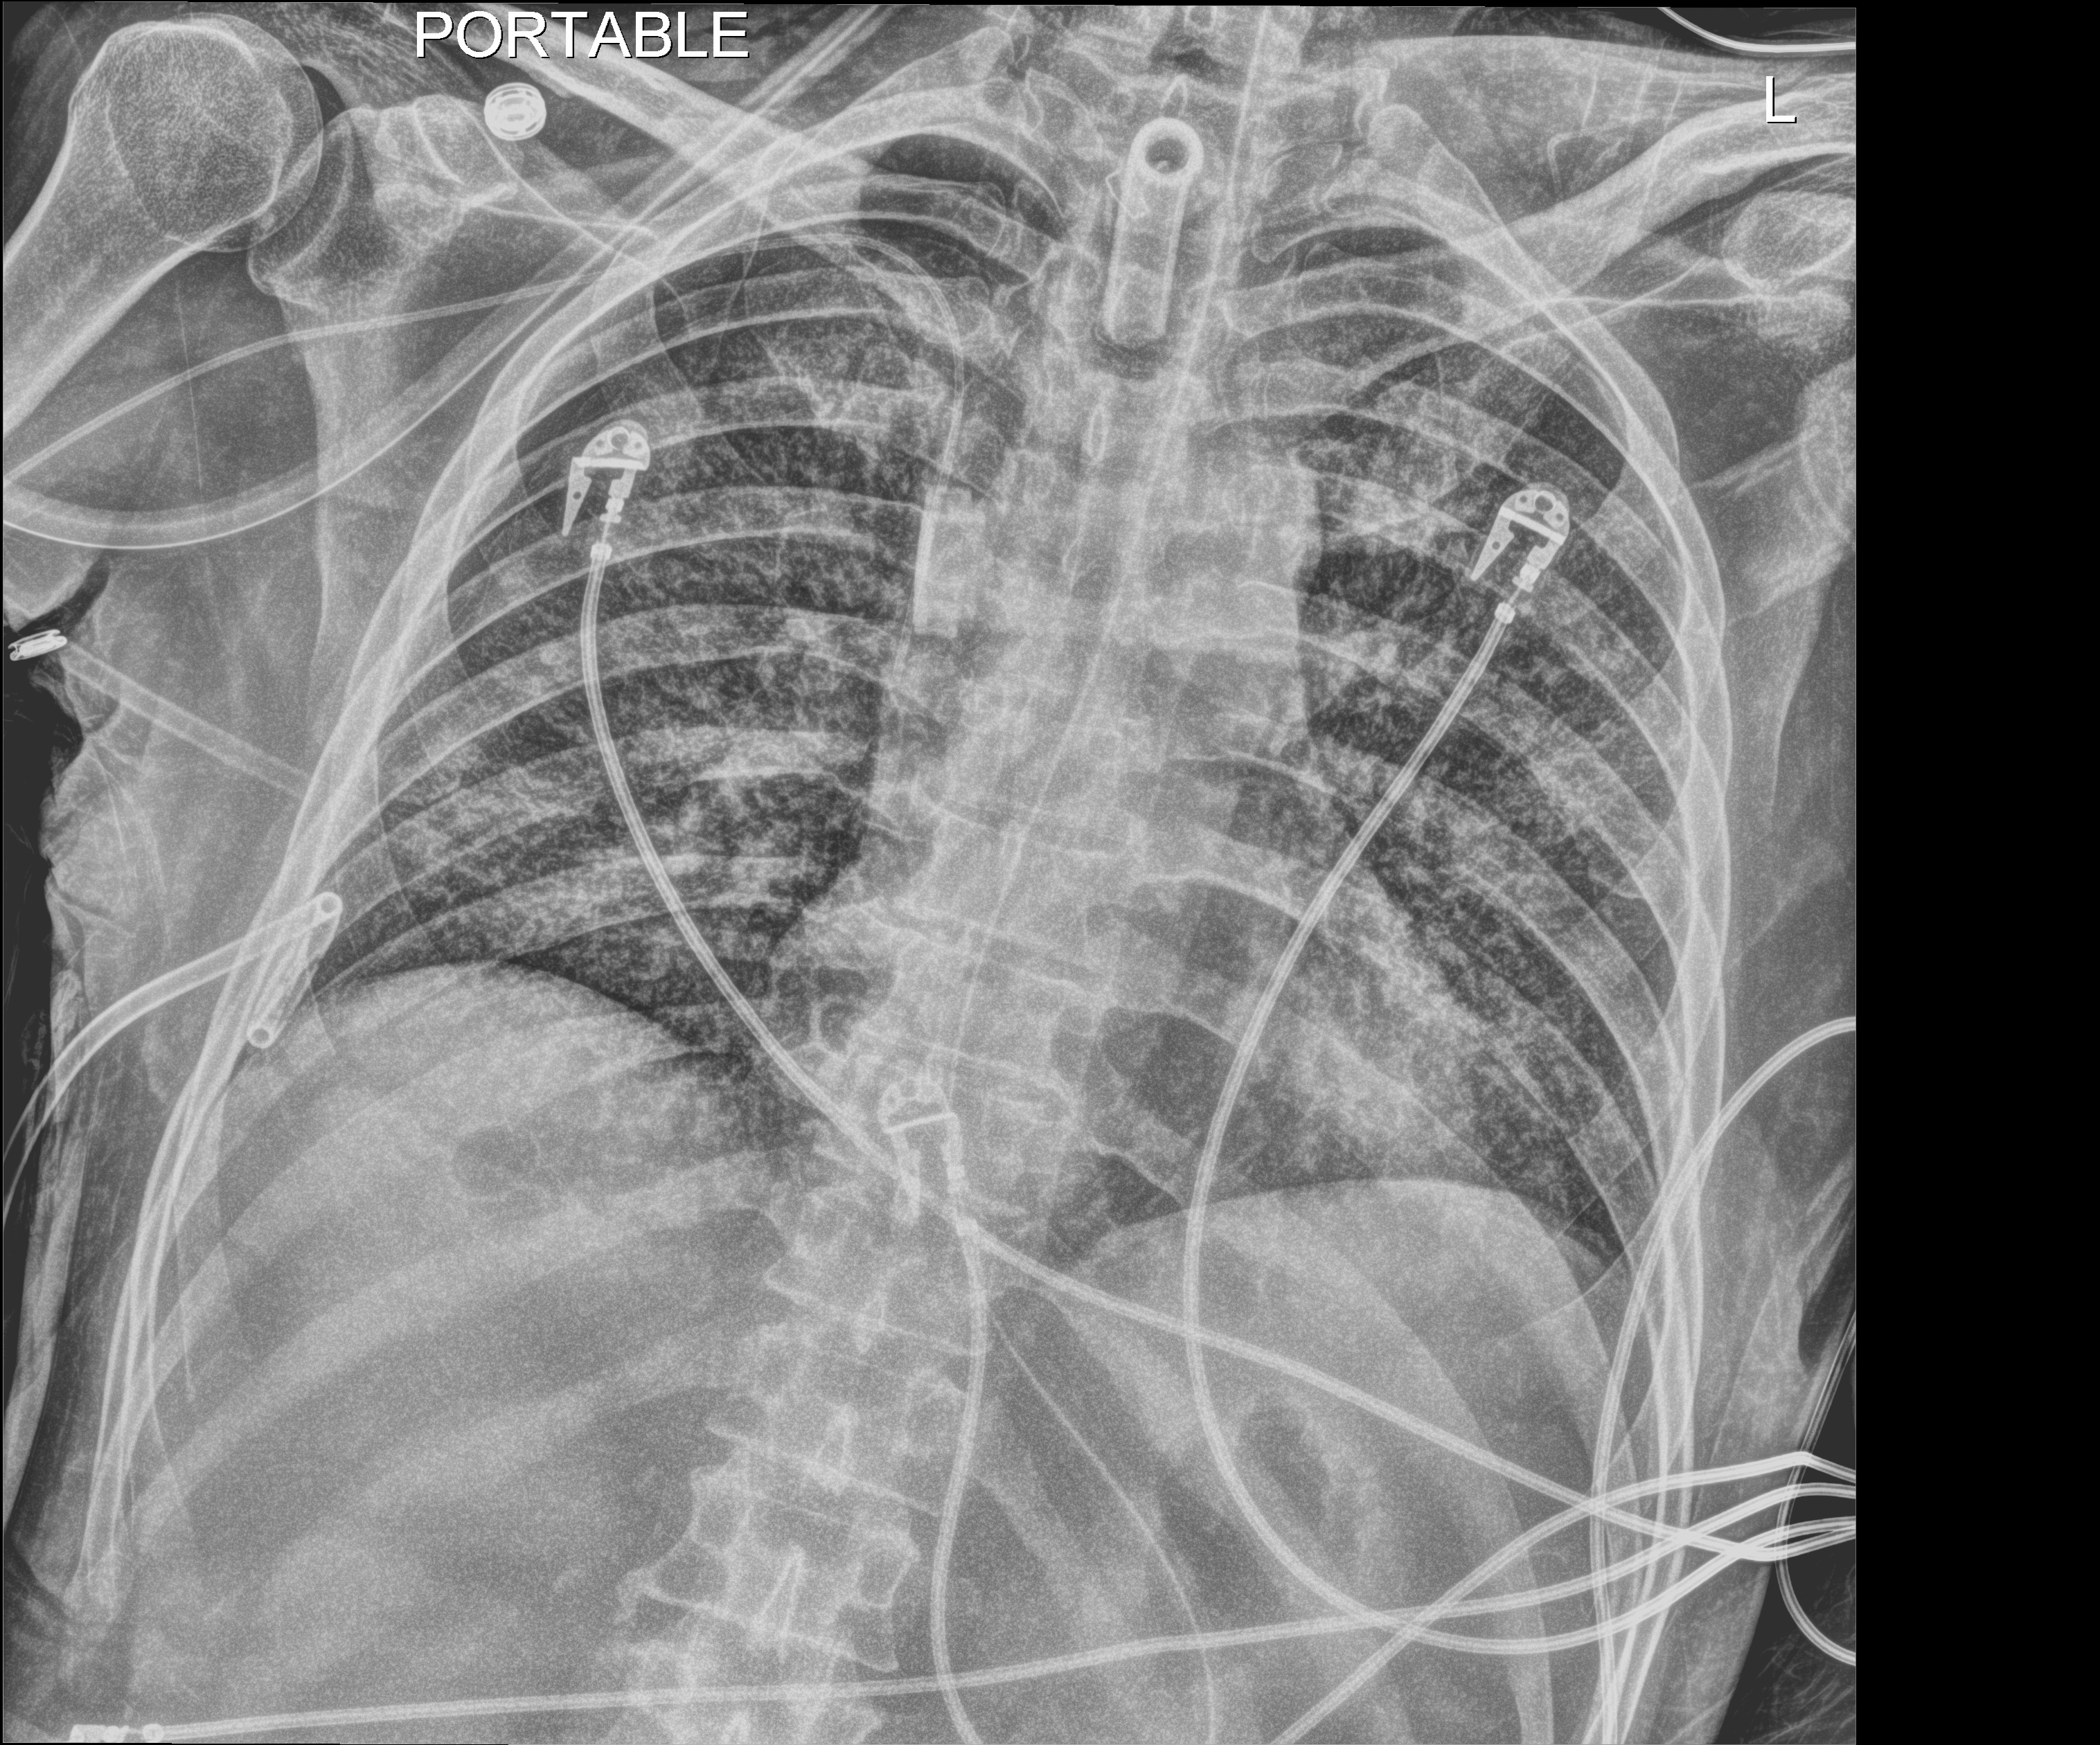
Portable chest radiograph; anteroposterior (AP) projection. Patient hospitalised with COVID-19; male, aged 18–59 years.
From the hospital-stay record, not from the radiograph (when in the stay this image was taken is not recorded): smoking status (admission record): never.